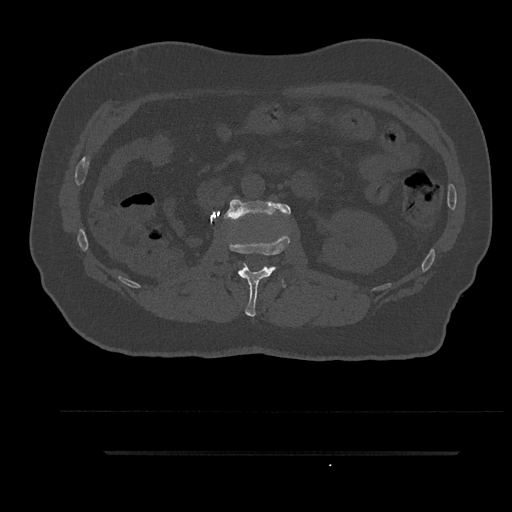
CT including the spine, one axial slice. Position 154 of 797 along the scan axis. Bone window (W 1800 / L 400 HU). 0.5 mm slice thickness. 512 × 512 image matrix. Patient: male, 63 years. From the clinical record (not read from this slice): primary cancer: renal; vertebrae with lytic lesions (as recorded): T8.
Annotated regions visible in this slice (semi-automatically segmented with operator editing):
- L1 vertebra: bounding box (x1, y1, x2, y2) in pixels: (229, 234, 290, 317)
- L2 vertebra: (224, 199, 291, 220)